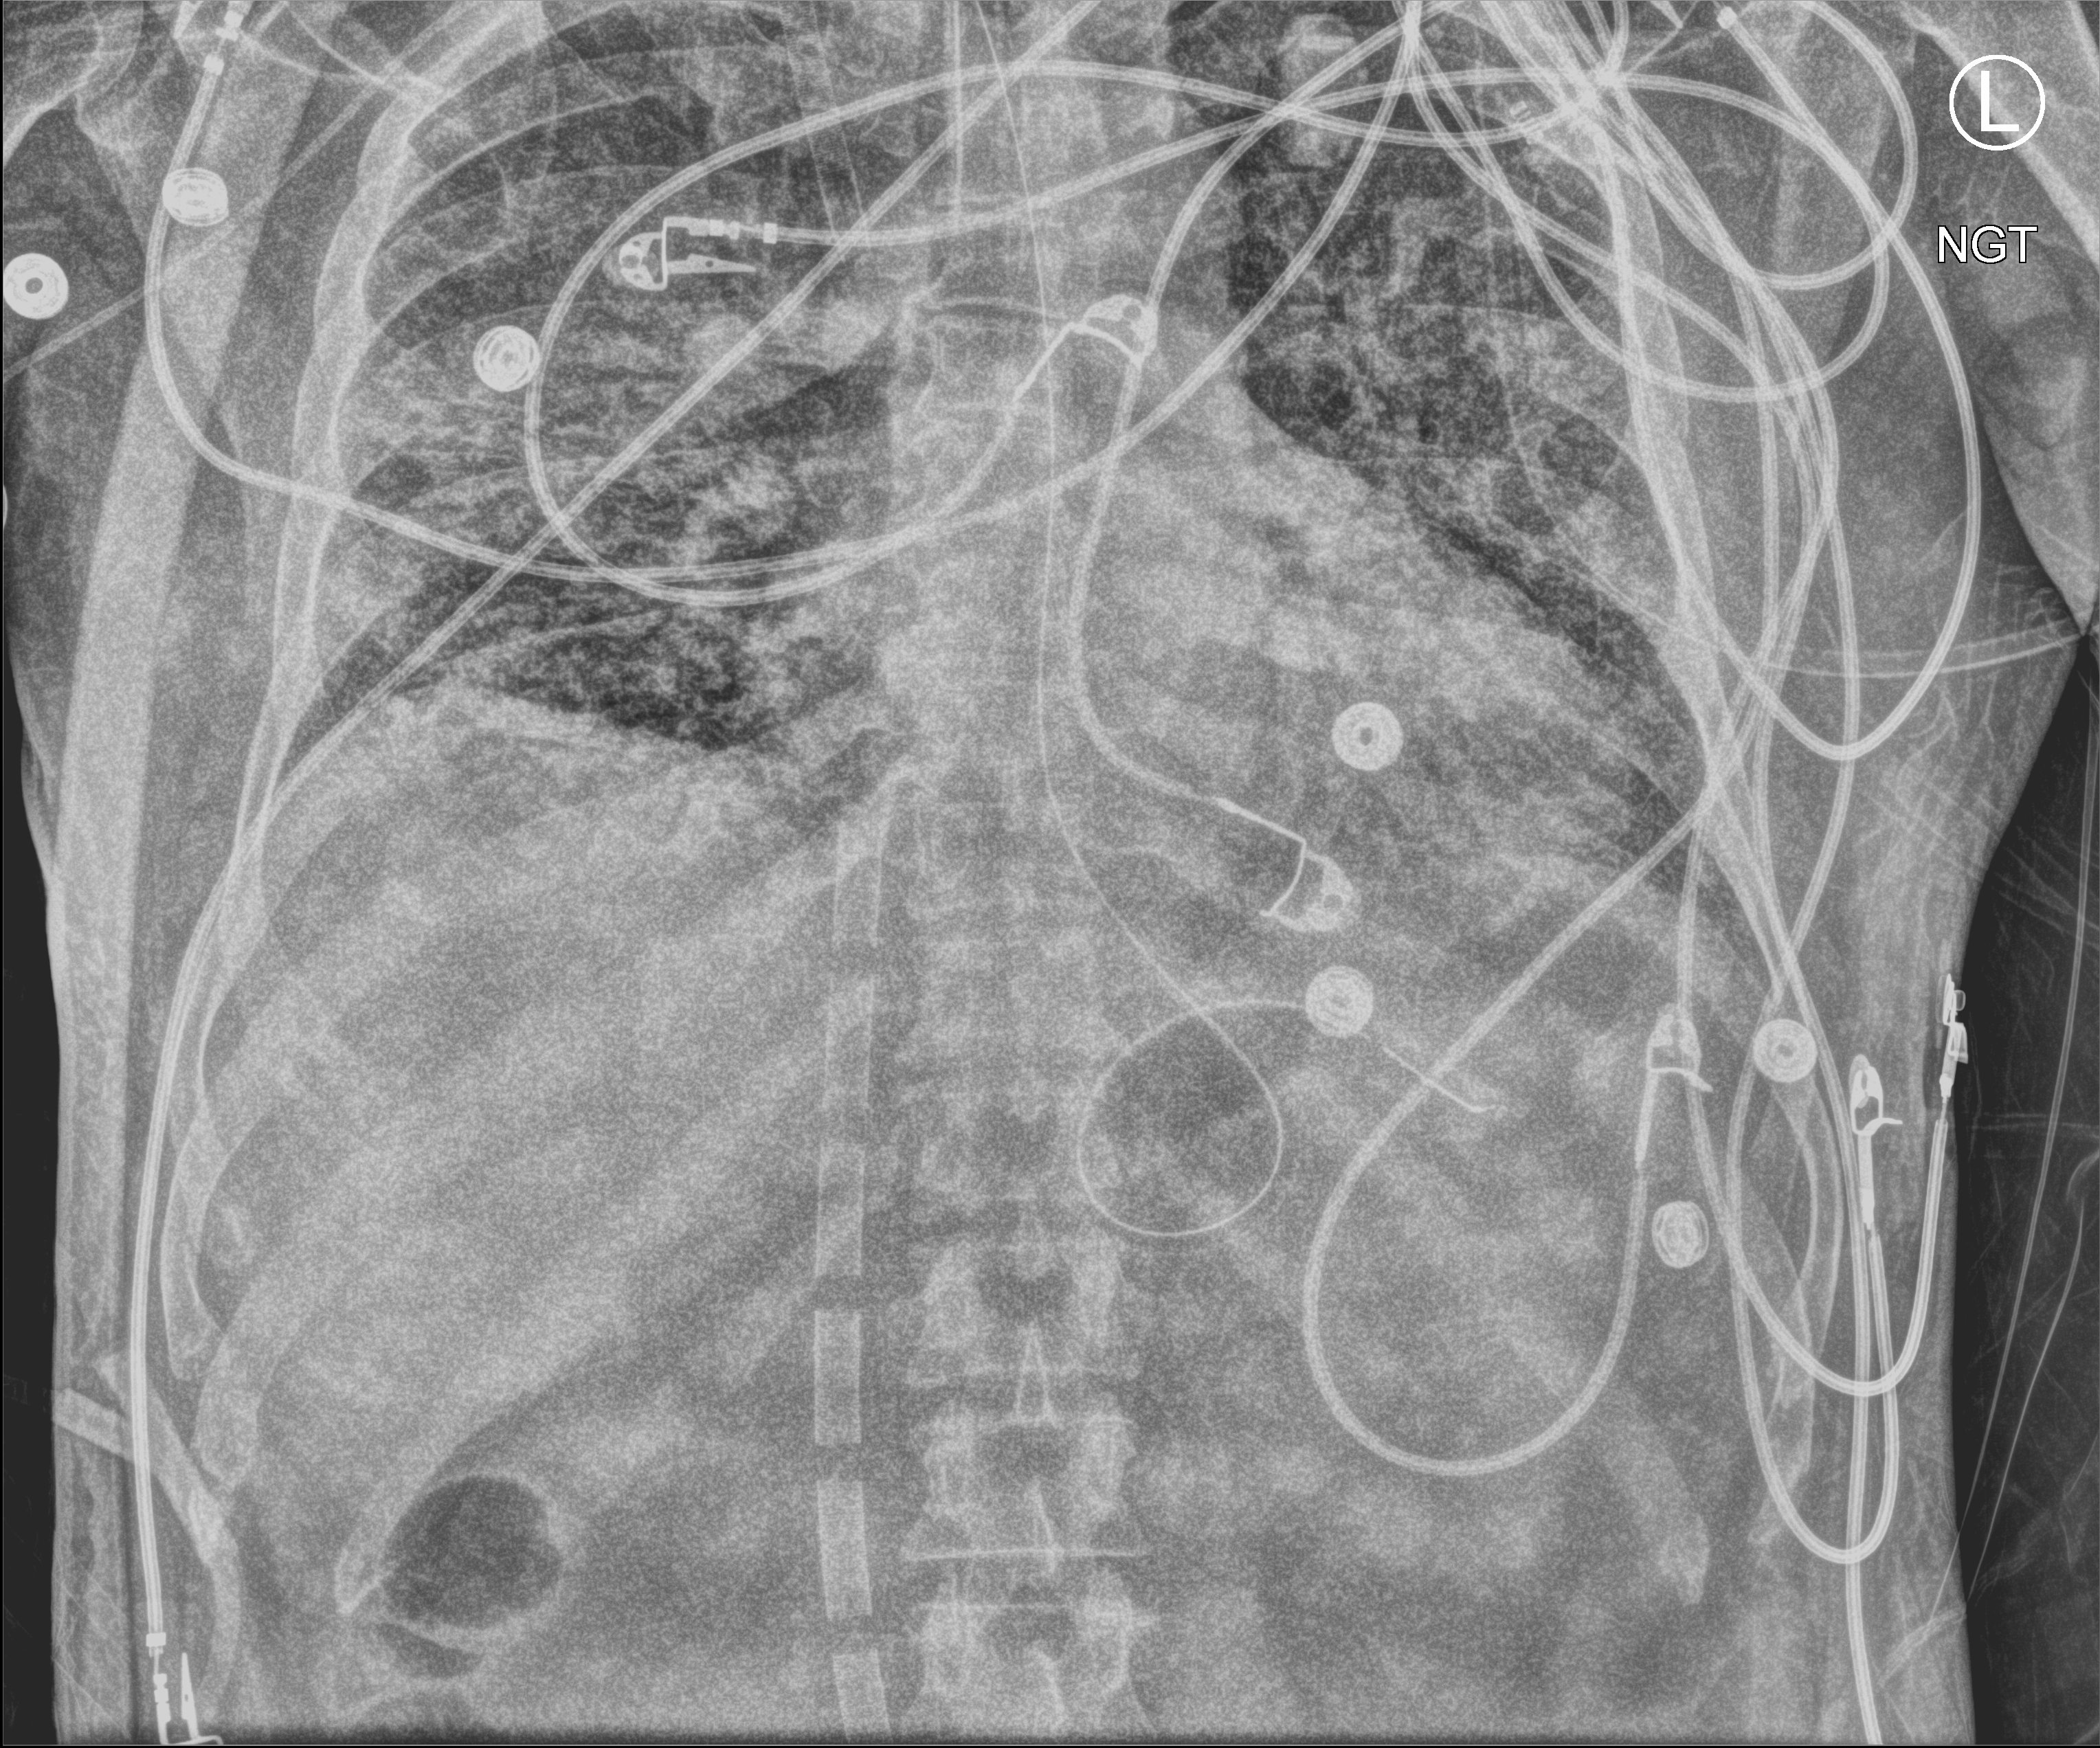
Chest X-ray (portable); anteroposterior (AP) projection. Patient hospitalised with COVID-19; male, aged 18–59 years.
Hospital-stay facts (about this admission, not read from this image; timing relative to this image not recorded):
- chronic kidney disease (admission record): no
- admitted to intensive care during this hospital stay: yes